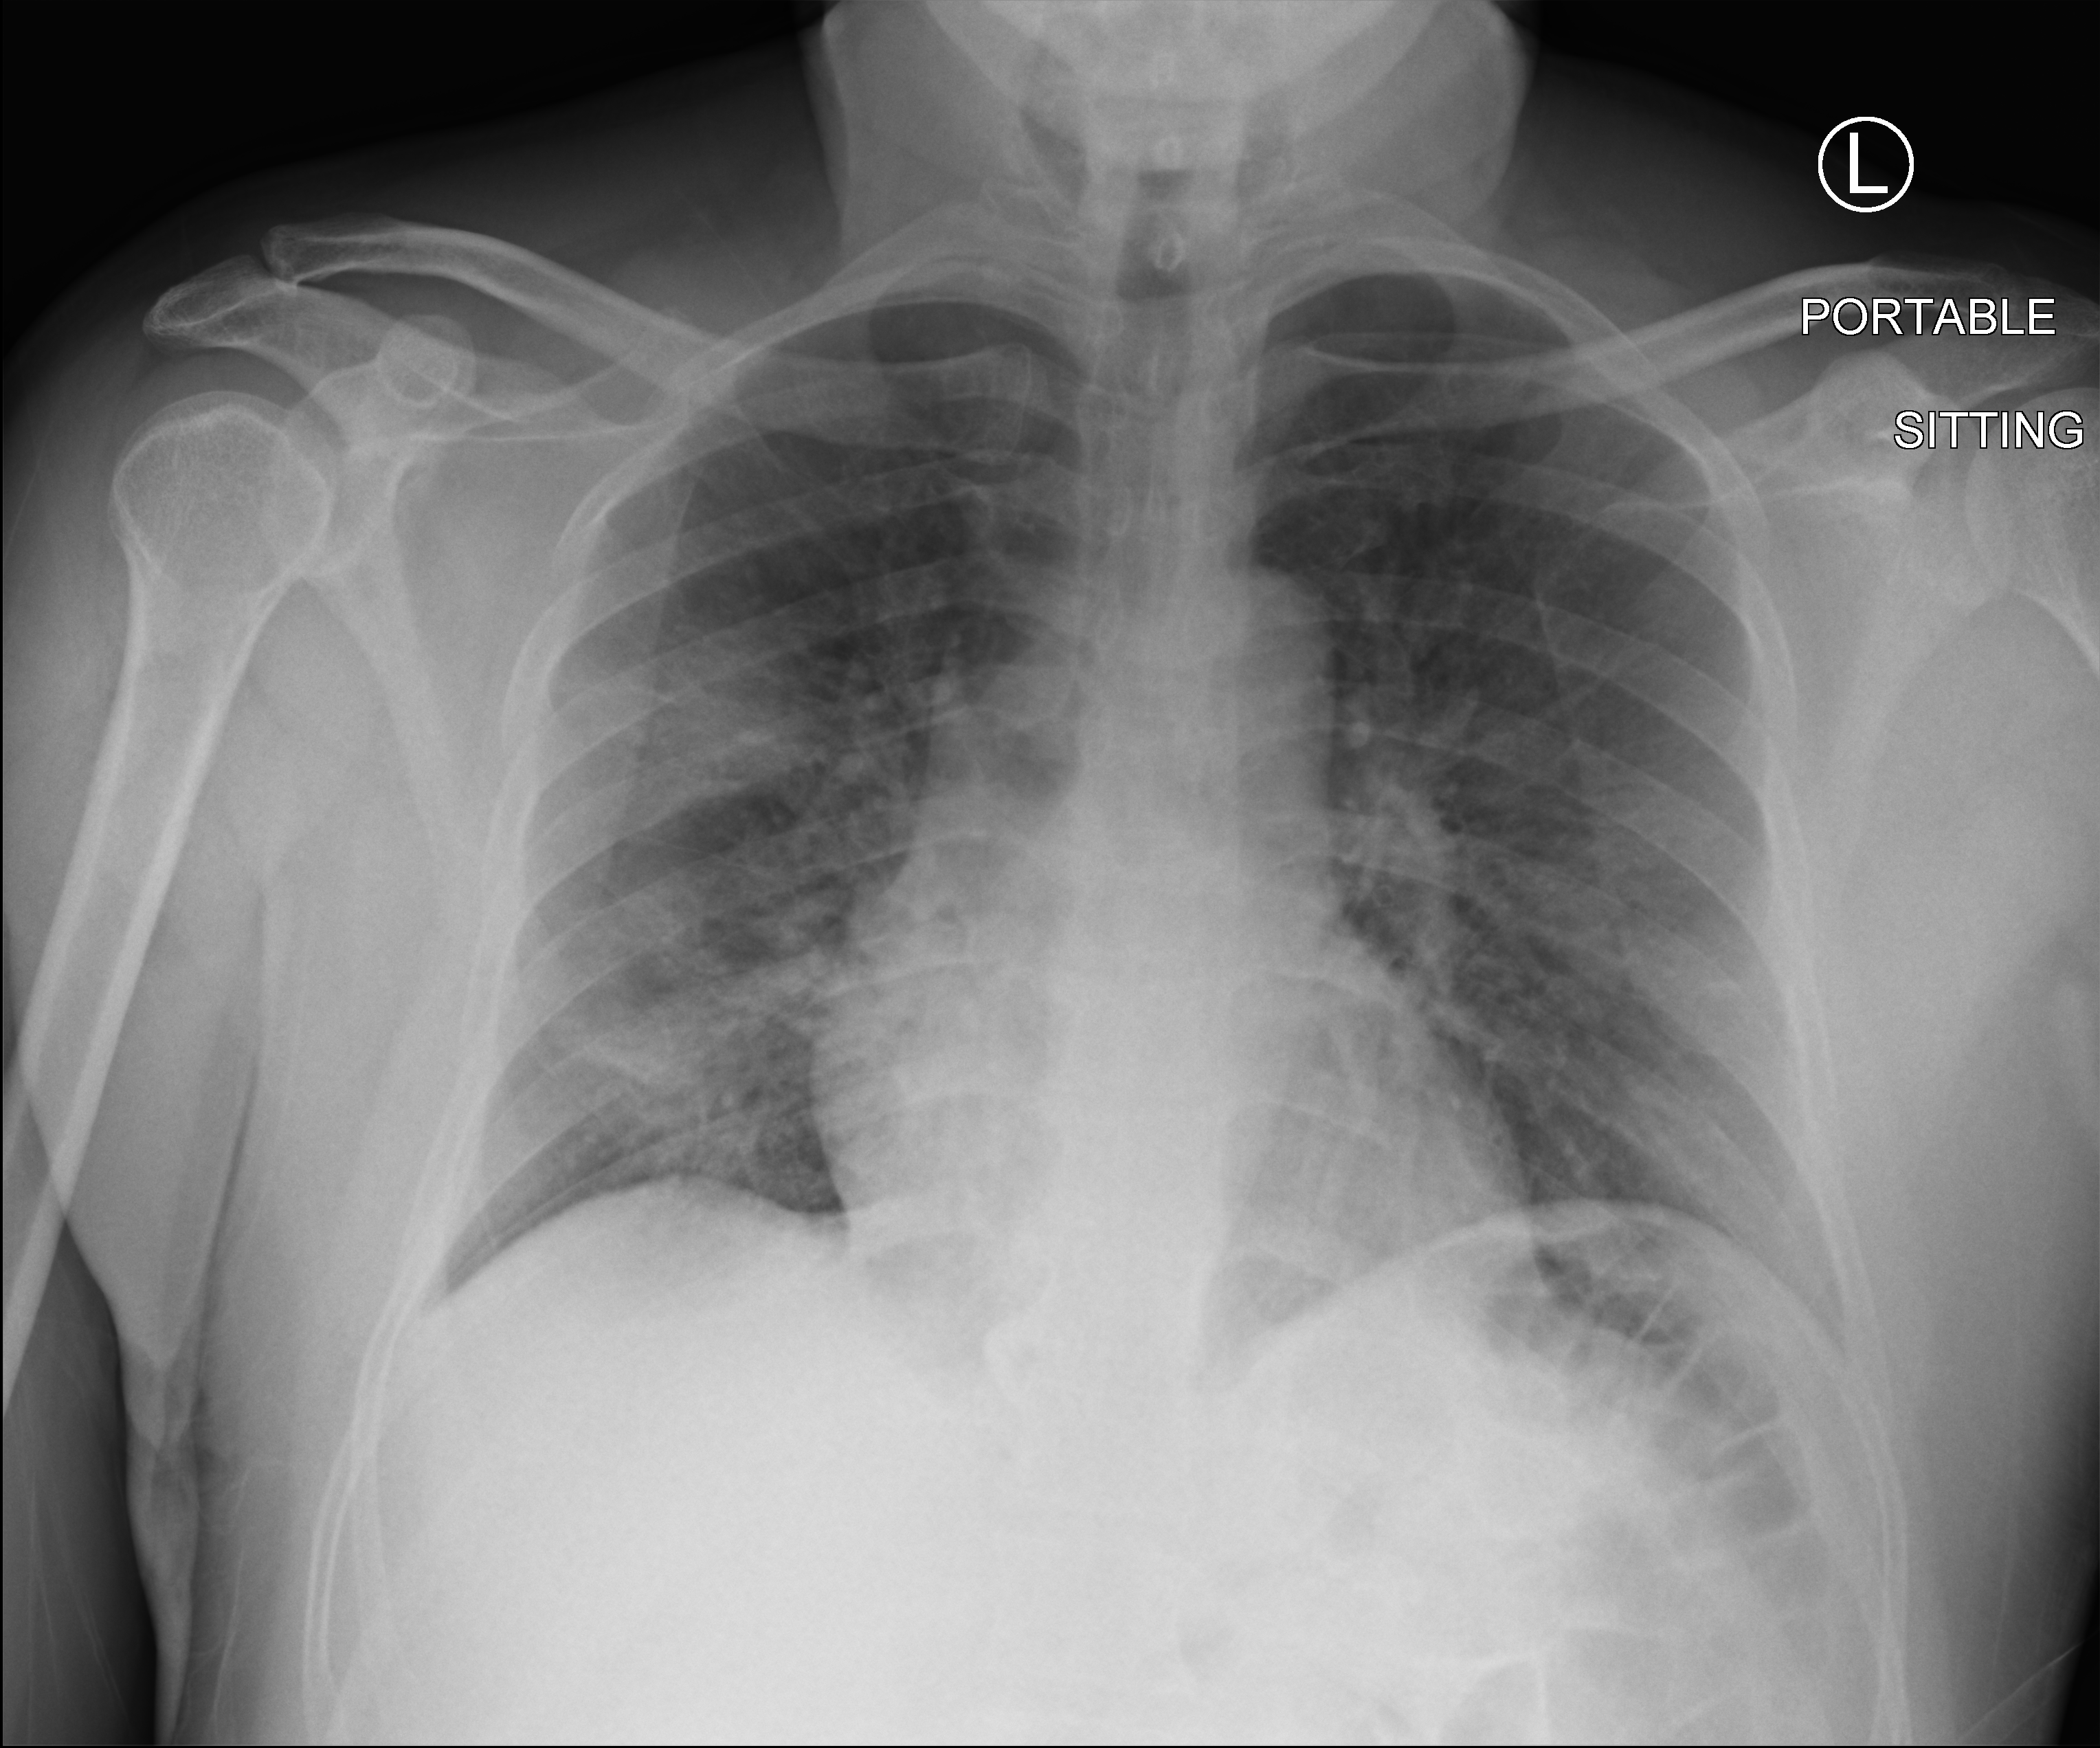
Bedside chest radiograph (computed radiography); anteroposterior (AP) projection. Patient hospitalised with COVID-19; male, aged 18–59 years.
Hospital-stay facts (about this admission, not read from this image; timing relative to this image not recorded): admitted to intensive care during this hospital stay: no; mechanically ventilated during this hospital stay: no.